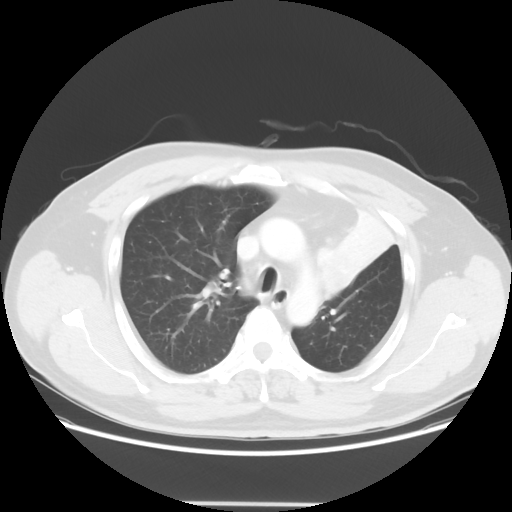
Chest CT, one axial slice. Slice 43 of 62 in the series (ordered by position). 120 kVp. Lung window (W 1500 / L -600 HU). 5 mm slice thickness. 512 × 512 image matrix. Patient: male, 49 years. From the clinical record (not read from this slice): clinical TNM (as recorded): T3 N3 M1c.
Annotated regions visible in this slice (bounding box drawn by a radiologist):
- lung tumour (recorded histology: squamous cell carcinoma): bounding box [x1, y1, x2, y2] px = [311, 244, 357, 301]